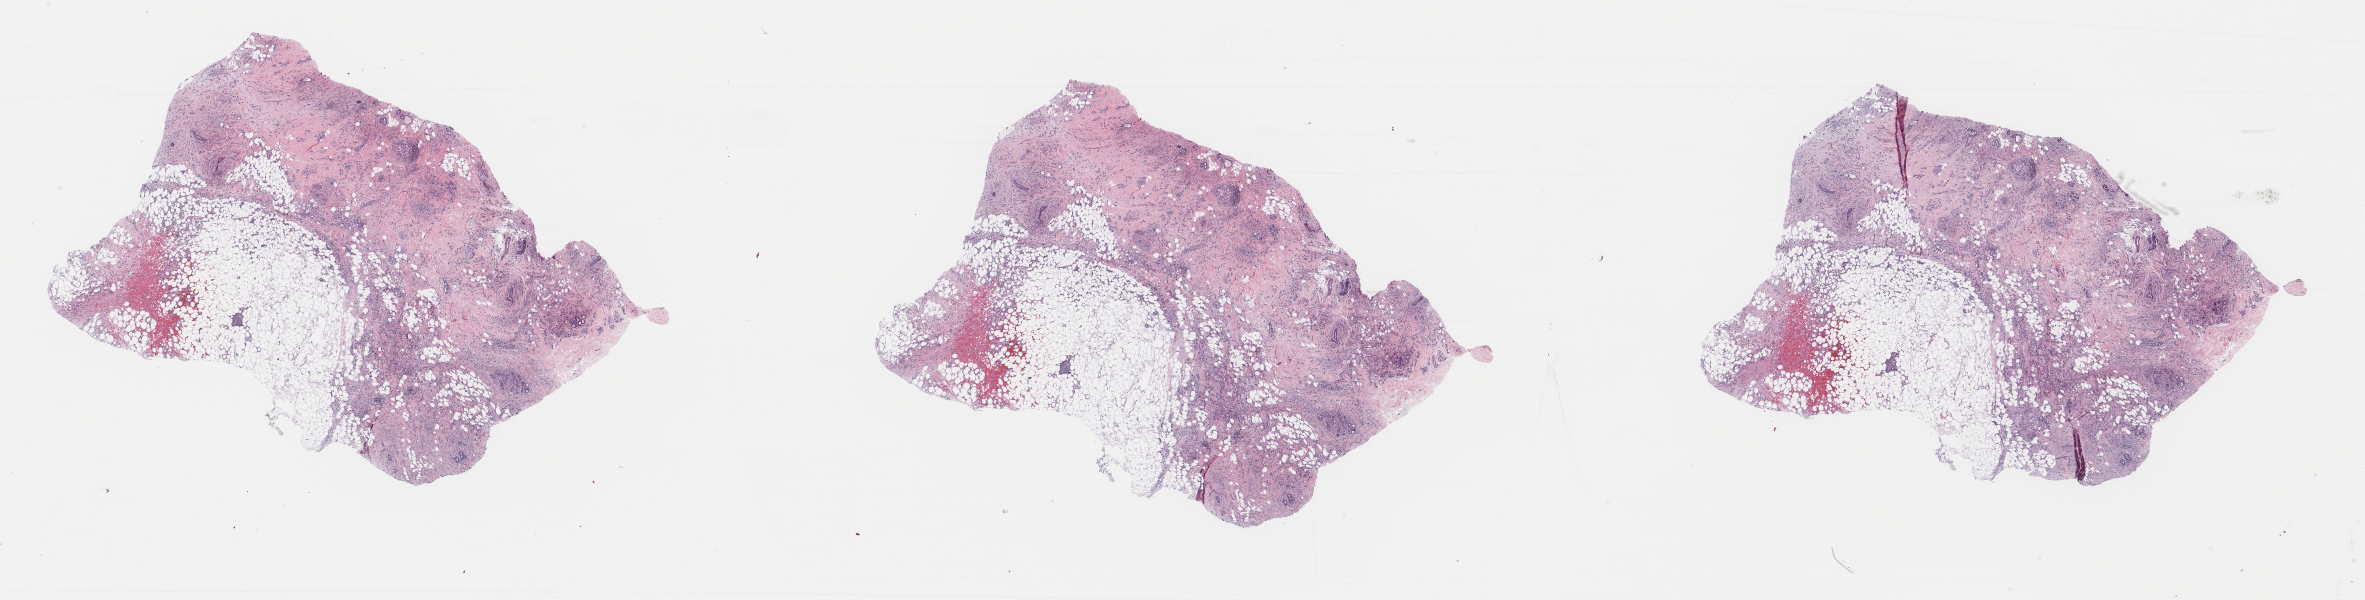
Hematoxylin and eosin (H&E) stained whole-slide image — low-resolution overview of the scanned area, about 37.3 x 9.5 mm (acquisition: 40x scan); FFPE section; breast, primary tumour sample. Female, age 78 years at initial diagnosis.
AJCC pathologic stage: IIA. Pathologic diagnosis: Infiltrating duct and lobular carcinoma.